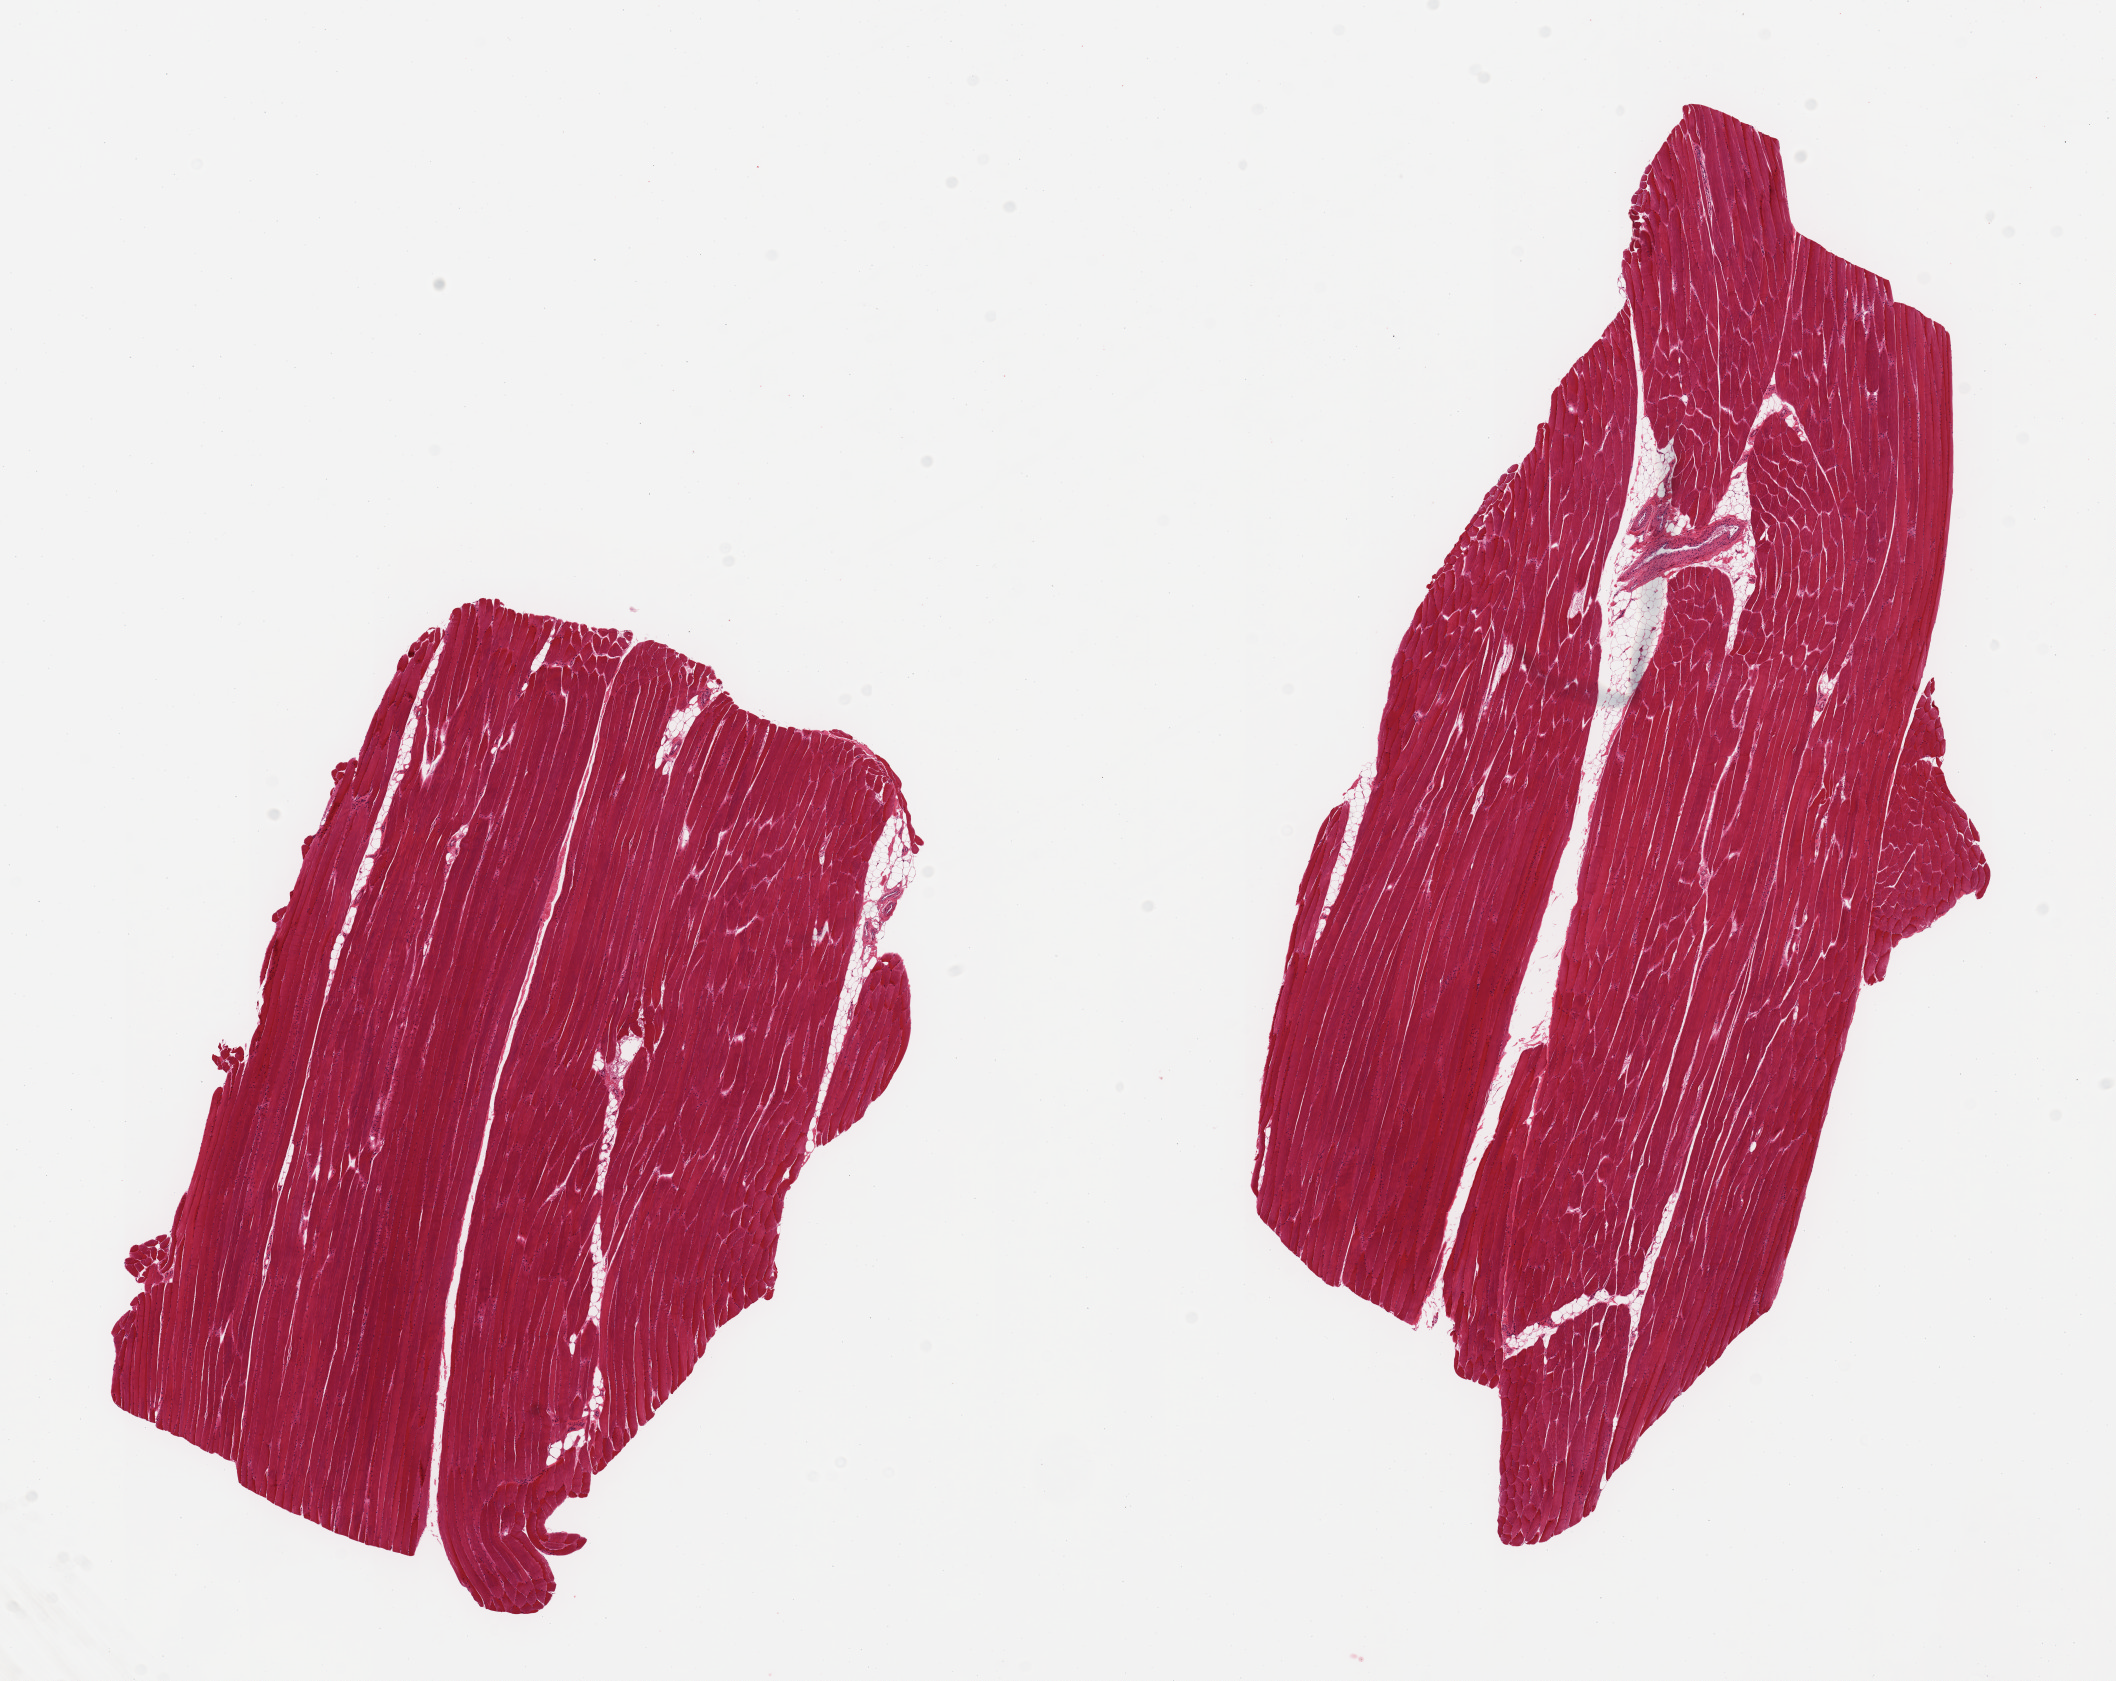
H&E whole-slide image, a low-resolution overview of the entire scanned area, about 16.7 x 13.3 mm; PAXgene-fixed, paraffin-embedded tissue; target tissue: skeletal muscle; tissue donor sample. Male donor.
• reviewer comment on this tissue sample: 2 pieces, ~10% interstitial fat/vascular elements